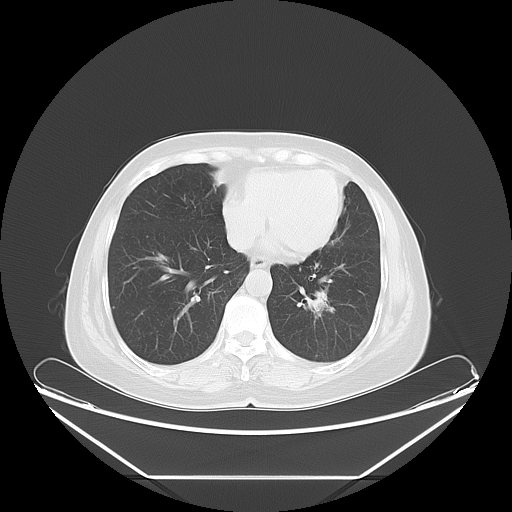
Chest CT, one axial slice. Slice 22 of 61 in the series (ordered by position). Reconstruction kernel LUNG. 120 kVp. Lung window (W 1500 / L -600 HU). 5 mm slice thickness. 512 × 512 image matrix, field of view 451 × 451 mm. Patient: female, 63 years. From the clinical record (not read from this slice): clinical TNM (as recorded): T1c N0 M0.
Outlined on this slice (bounding box drawn by a radiologist):
- lung tumour (recorded histology: adenocarcinoma): box from (x=310, y=288) to (x=332, y=324) px